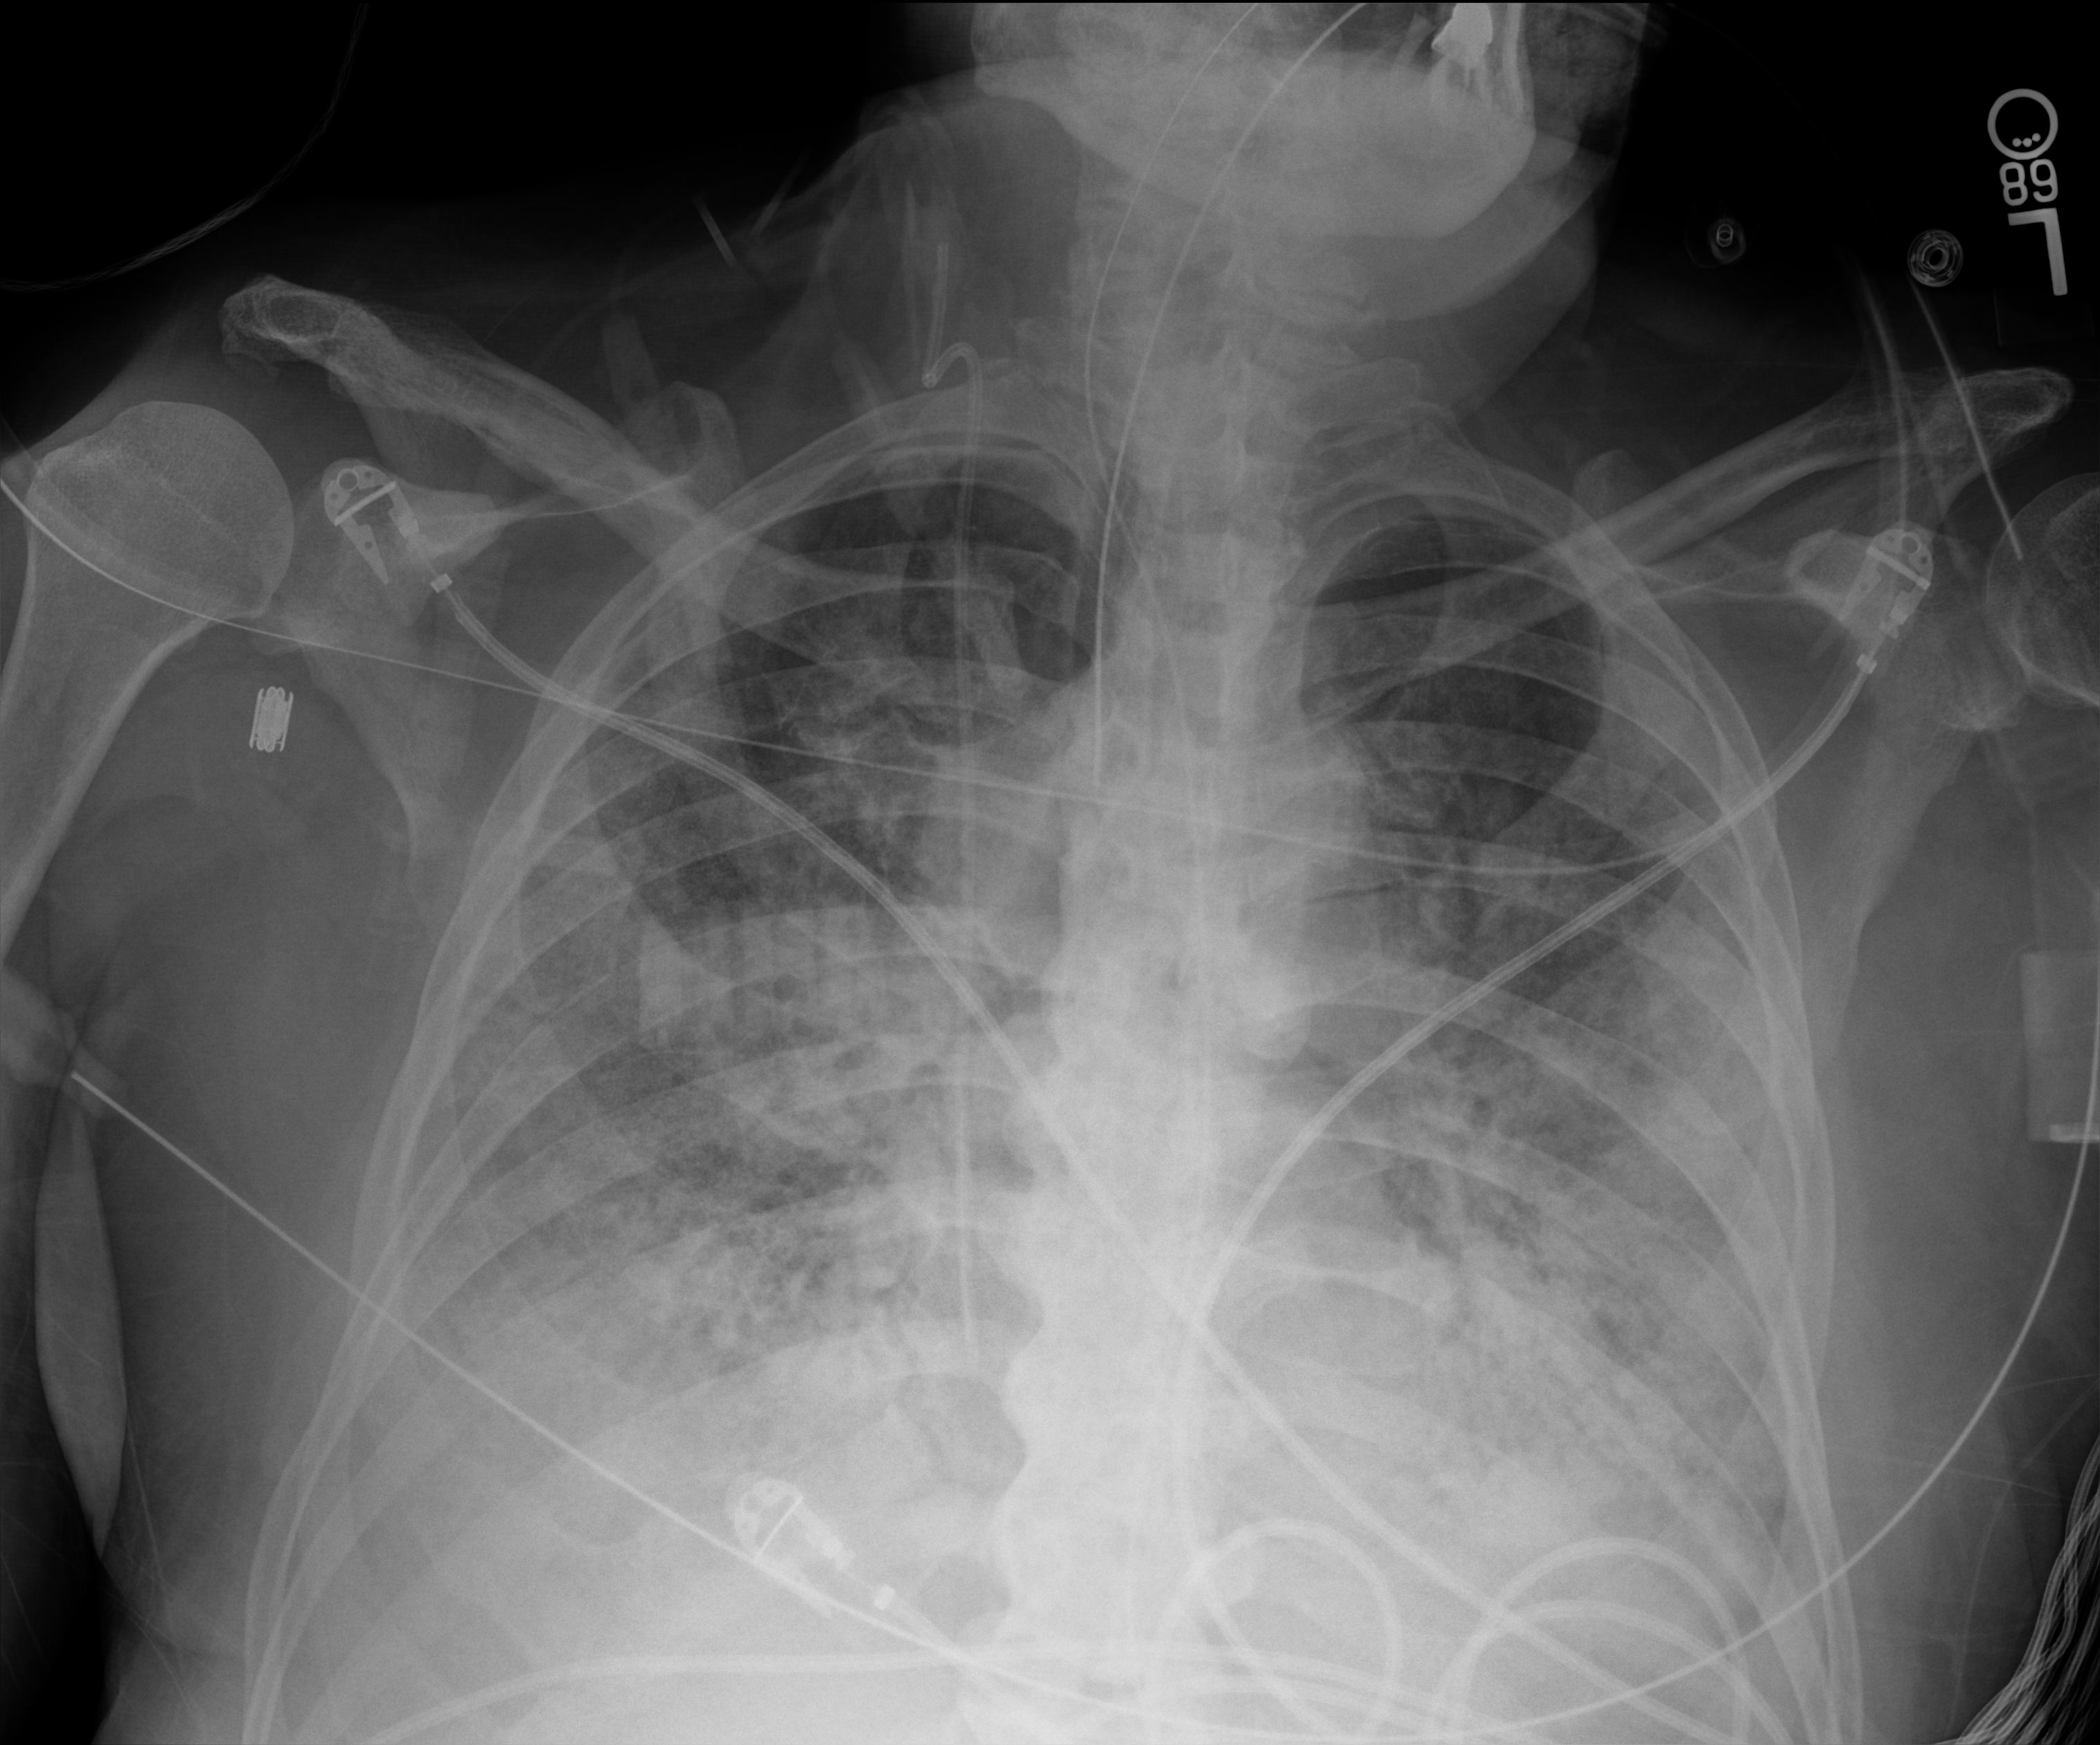
Chest X-ray (portable). Patient hospitalised with COVID-19; male, aged 75–90 years.
From the hospital-stay record, not from the radiograph (when in the stay this image was taken is not recorded):
- COPD (admission record): no
- admitted to intensive care during this hospital stay: yes
- diabetes (admission record): no